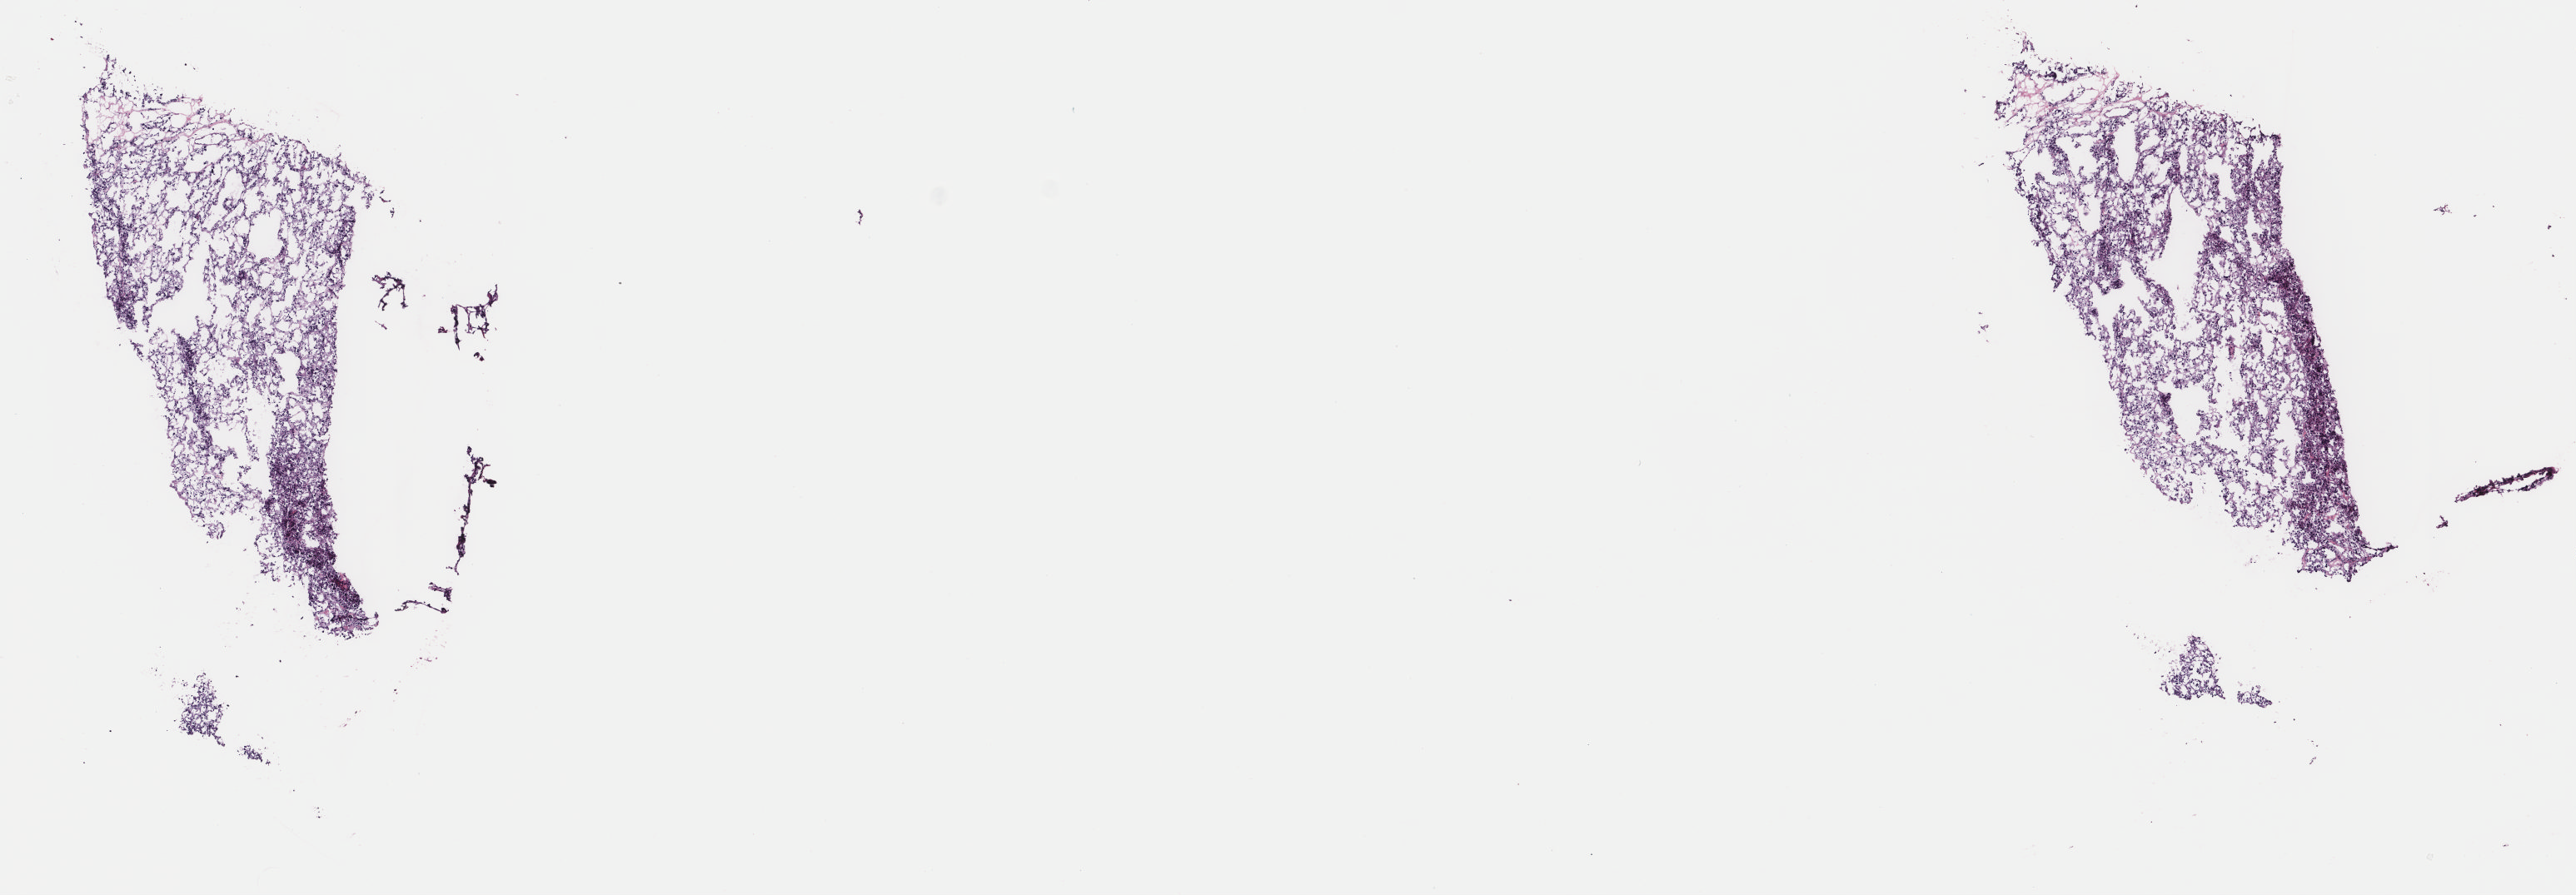
Whole-slide histology image, Hematoxylin and eosin (H&E) stained, shown as a low-resolution overview of the whole scanned area (about 12.3 x 4.3 mm), frozen section from the top of the tissue portion, primary tumour sample from the adrenal gland. Female, age 30 years at initial diagnosis. Slide review estimates, as recorded: tumour cells 80%, tumour nuclei 80%.
Pathologic diagnosis: Pheochromocytoma, NOS.